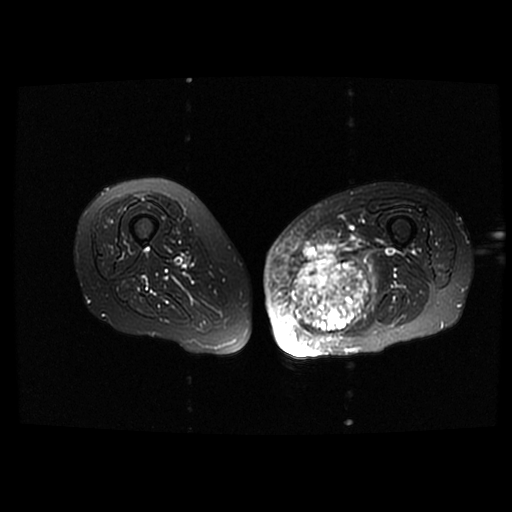
MRI of an extremity soft-tissue mass, one axial slice; position 34 of 42 along the scan axis; T2-weighted fat-saturated; 6 mm slice thickness; 512 × 512 image matrix, field of view 420 × 420 mm. Female patient. Case-level facts recorded for this patient, not image findings: histological type: pleomorphic leiomyosarcoma; grade: high; site of the primary tumour: left thigh.
Annotated regions visible in this slice (outlined manually by an expert reader):
- gross tumour volume including surrounding oedema: bounding box [x1, y1, x2, y2] px = [289, 243, 376, 334]
- gross tumour volume (mass): [289, 243, 370, 335]